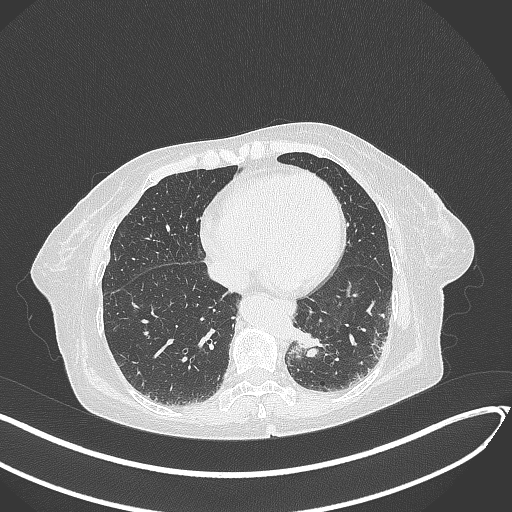
Chest CT, one axial slice. Position 66 of 324 along the scan axis. Reconstruction kernel B70f. 120 kVp. Lung window (W 1500 / L -600 HU). 1 mm slice thickness. 512 × 512 image matrix, field of view 400 × 400 mm. Female patient, age 82 years. From the clinical record (not read from this slice): clinical TNM (as recorded): T1b N0 M1.
Structures marked on this image (rectangle marked by the reading radiologist):
- lung tumour (recorded histology: adenocarcinoma): box from (x=294, y=328) to (x=322, y=357) px